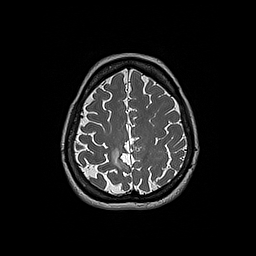
Brain MRI from a brain-tumour surgery series, one axial slice; position 55 of 192 along the scan axis; 256 × 256 image matrix. From the clinical record (not read from this slice): histopathology: Oligodendroglioma; WHO grade: 2; IDH mutation: yes; tumour location: Right Parietal.
Outlined on this slice (manually delineated by an expert):
- tumour: bounding box [x1, y1, x2, y2] px = [111, 148, 122, 170]